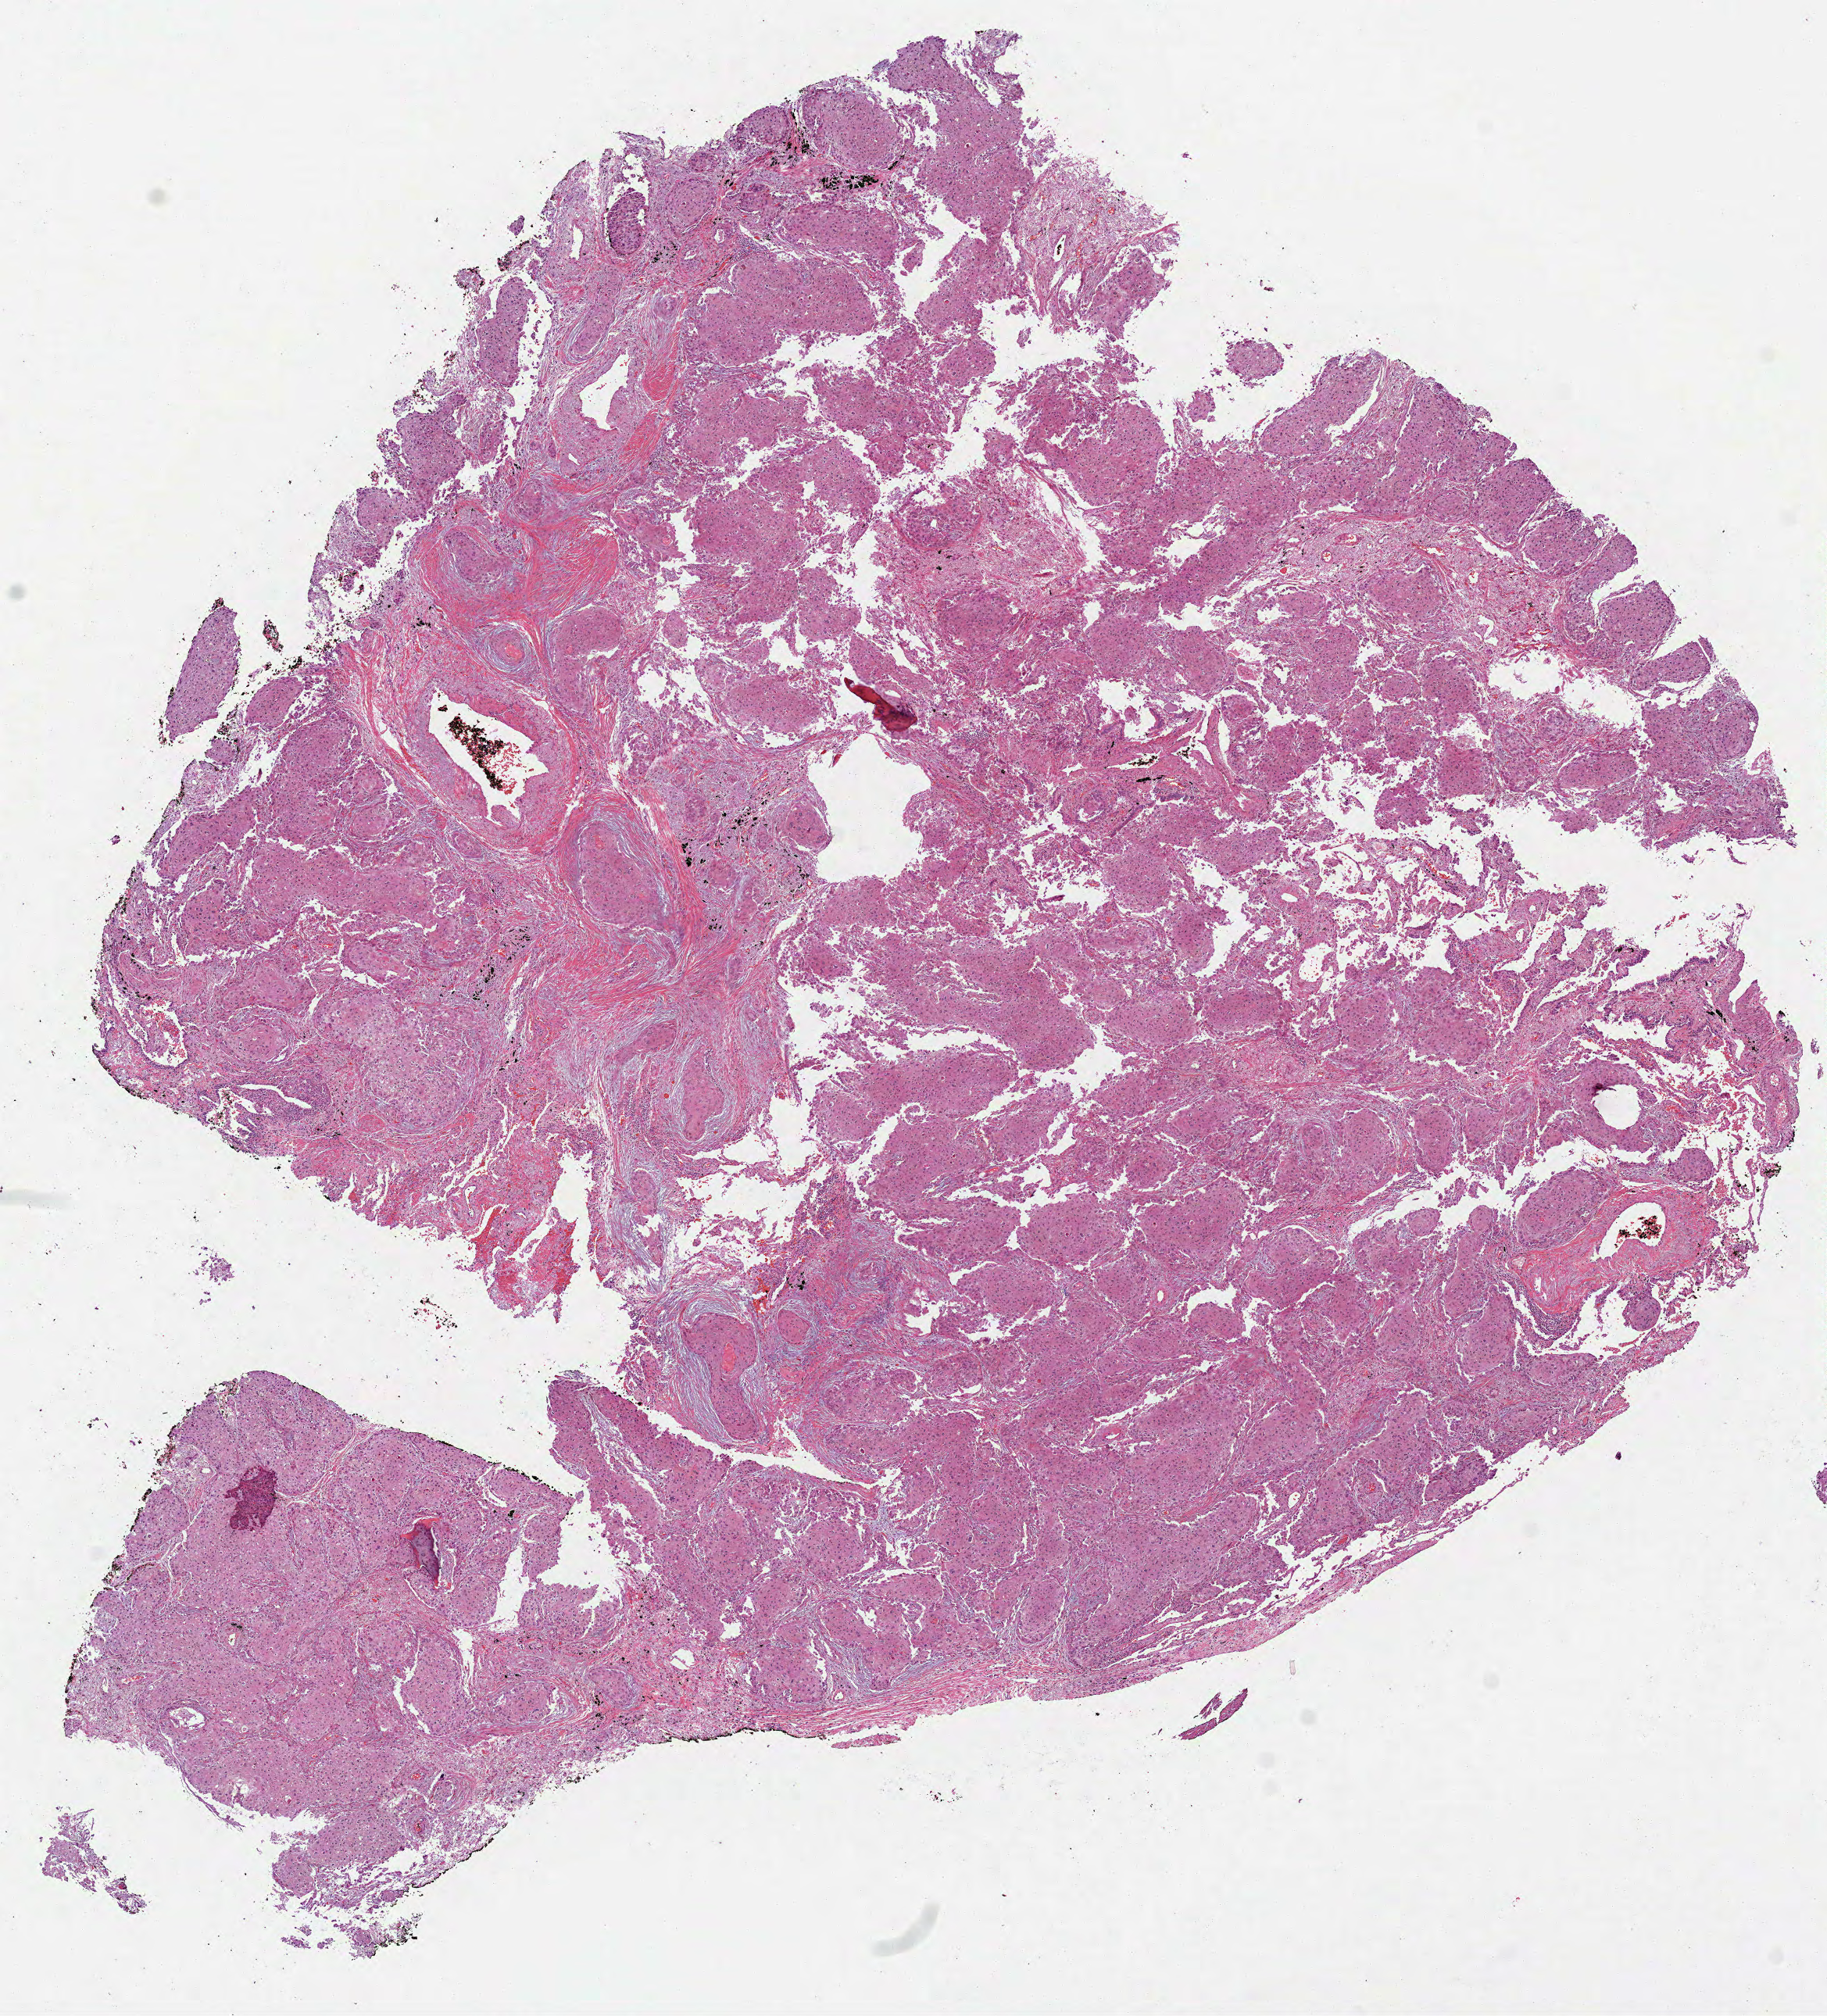
Digitized Hematoxylin and eosin (H&E) stained tissue section (whole slide), a low-resolution overview of the entire scanned area, about 9.4 x 10.4 mm, formalin-fixed paraffin-embedded (FFPE) diagnostic section, lung, primary tumour sample. Patient: male, age at initial diagnosis 84 years.
• laterality: right
• AJCC pathologic stage: IIB (7th edition)
• diagnosis: Squamous cell carcinoma, NOS (lower lobe, lung)